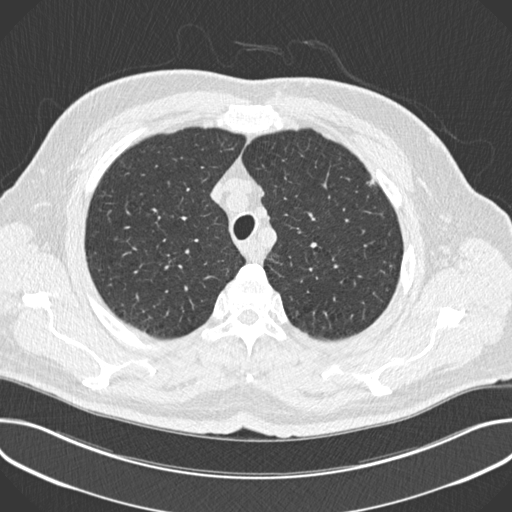
Chest CT (low-dose screening protocol), one axial image. First (baseline) screen. Lung window (W 1500 / L -600 HU). 2 mm slice thickness. Standard (soft-tissue) reconstruction kernel (B30f). 512 × 512 image matrix. Male participant, aged 63 years at enrolment.
• Expert-annotated lung lesion, box from (x=352, y=171) to (x=382, y=199) px.
• The screening reader recorded 2 non-calcified nodules or masses ≥4 mm on this exam (left upper lobe, left upper lobe); which of them this box marks is not recorded.
• Official screen result: positive, change unspecified: nodule(s) >= 4 mm or enlarging nodule(s), mass(es), or other non-specific abnormalities suspicious for lung cancer.
• Lung cancer was diagnosed 174 days after this screen: adenocarcinoma, NOS, left upper lobe, poorly differentiated (G3), stage IIIA (AJCC 6th edition), 11 mm at pathology.